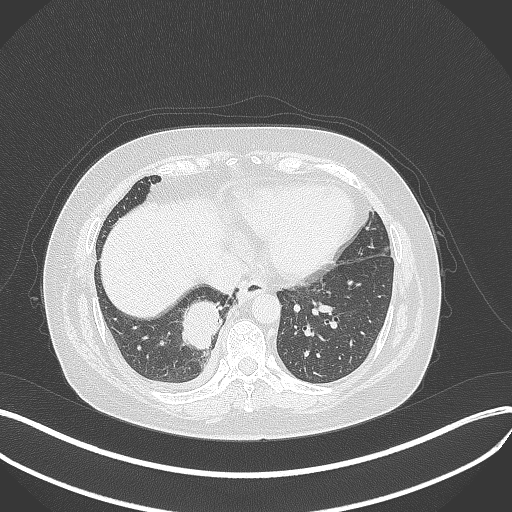
Chest CT, one axial slice. Position 107 of 381 along the scan axis. 120 kVp. Lung window (W 1500 / L -600 HU). 1 mm slice thickness. 512 × 512 image matrix. Patient: female, 56 years. From the clinical record (not read from this slice): clinical TNM (as recorded): T2b N1 M0; histopathological grade: G3.
Outlined on this slice (bounding box drawn by a radiologist):
- lung tumour (recorded histology: small cell carcinoma): box from (x=181, y=293) to (x=223, y=351) px